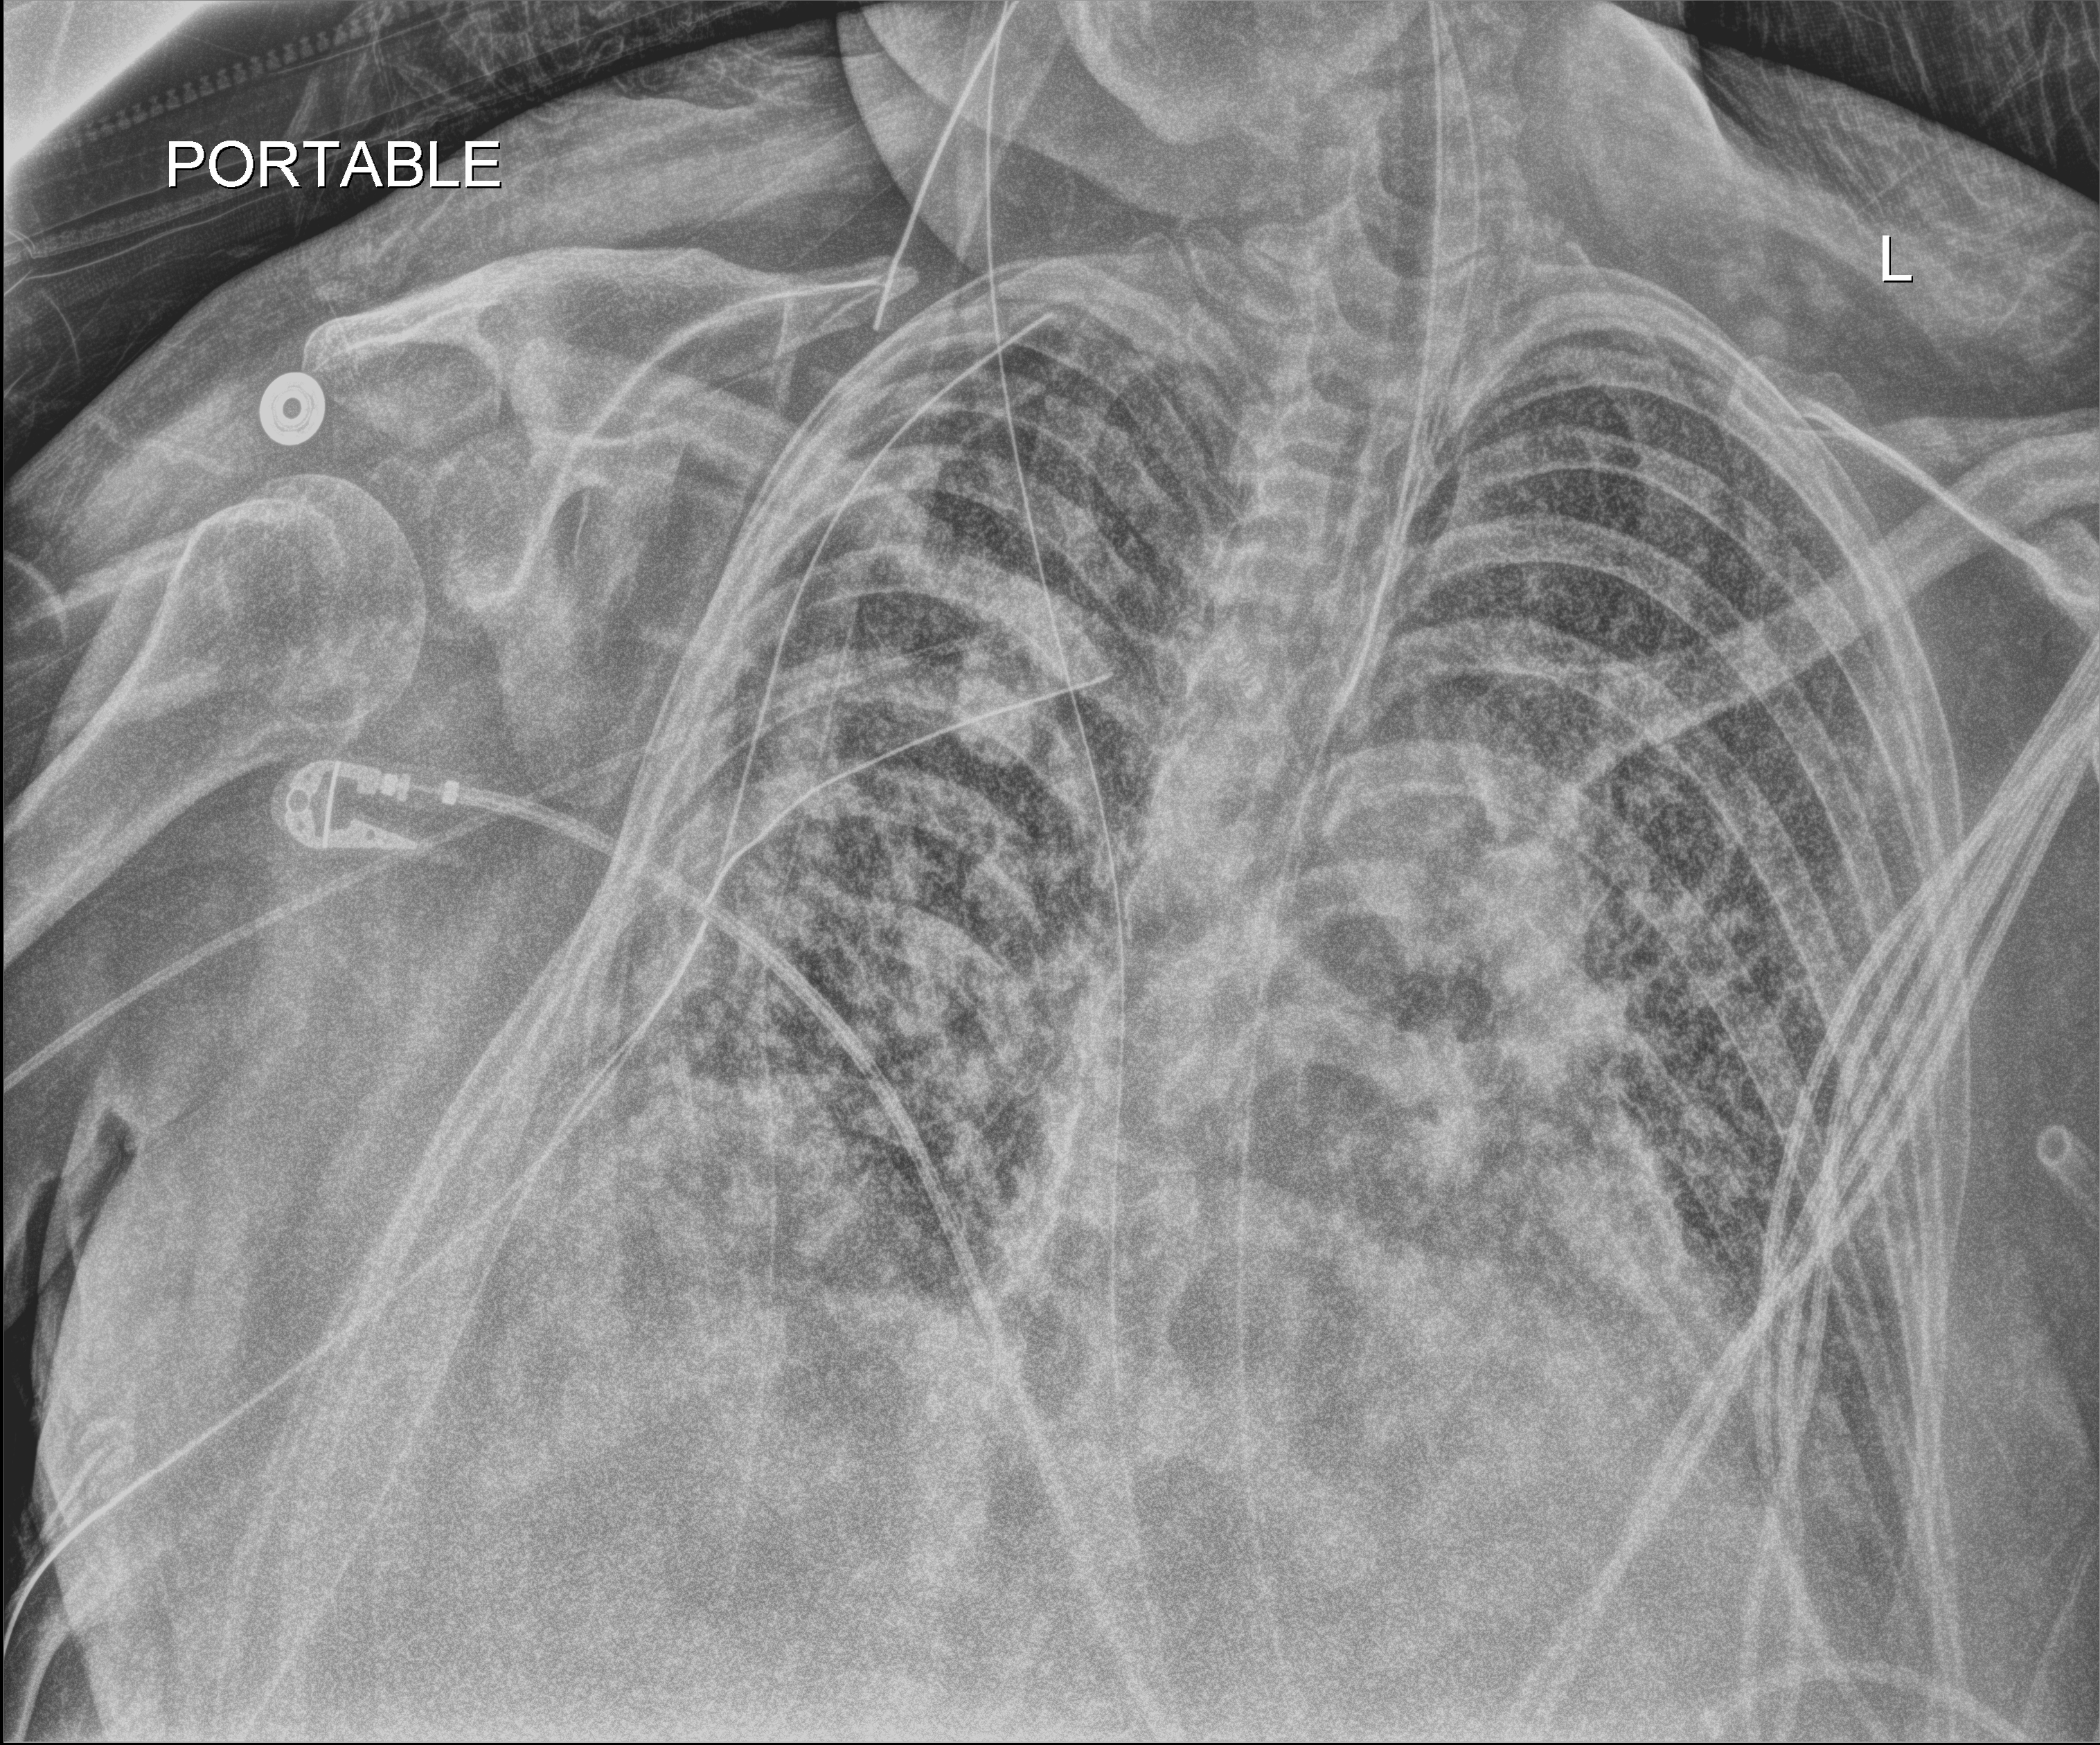
Chest X-ray (portable). Patient hospitalised with COVID-19, aged 18–59 years.
From the hospital-stay record, not from the radiograph (when in the stay this image was taken is not recorded): chronic kidney disease (admission record): no; mechanically ventilated during this hospital stay: yes; admitted to intensive care during this hospital stay: yes.